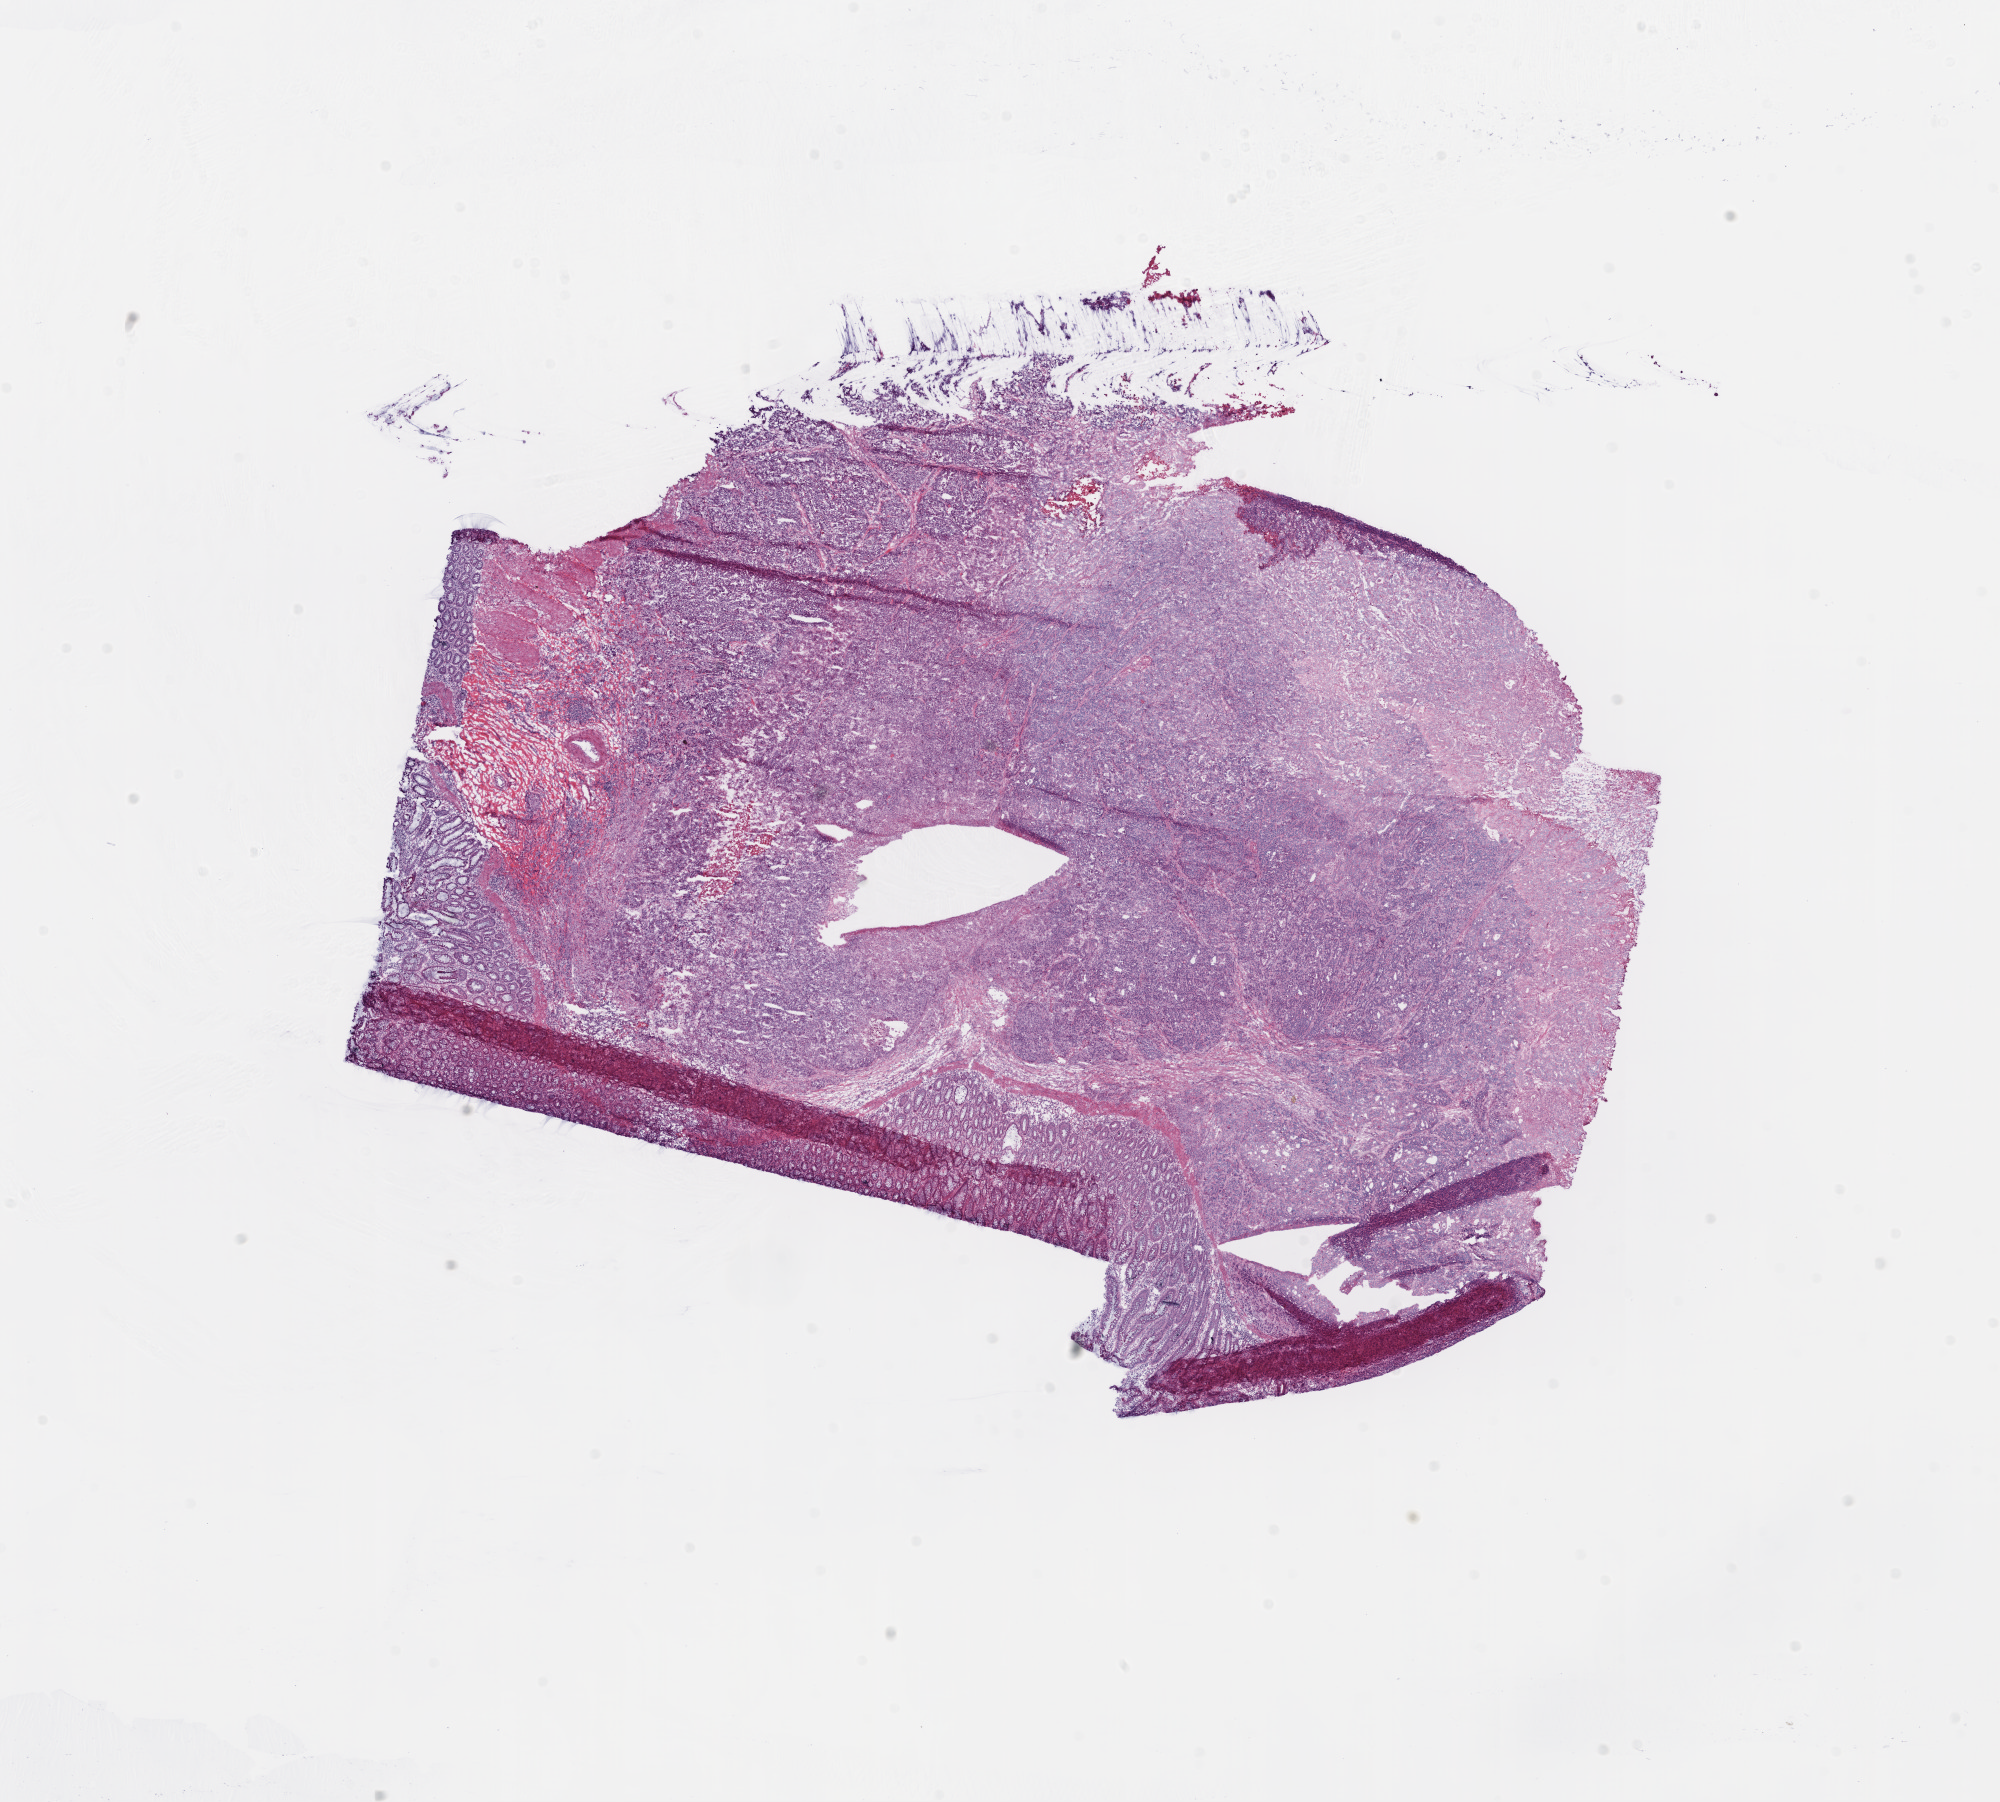
Digitized Hematoxylin and eosin (H&E) stained tissue section (whole slide), whole scanned area (about 16.0 x 14.5 mm, from a 20x scan) shown as a low-resolution overview; frozen section from the top of the tissue portion; sample: primary tumour, colon. Female, age 84 years at initial diagnosis. Composition of this section per pathologist review: tumour nuclei 80%, normal cells 15%, stromal cells 5%, necrosis 5%.
AJCC pathologic stage: III. Diagnosis: Adenocarcinoma with neuroendocrine differentiation. Lymph nodes positive (case pathology): 5 of 15 examined.